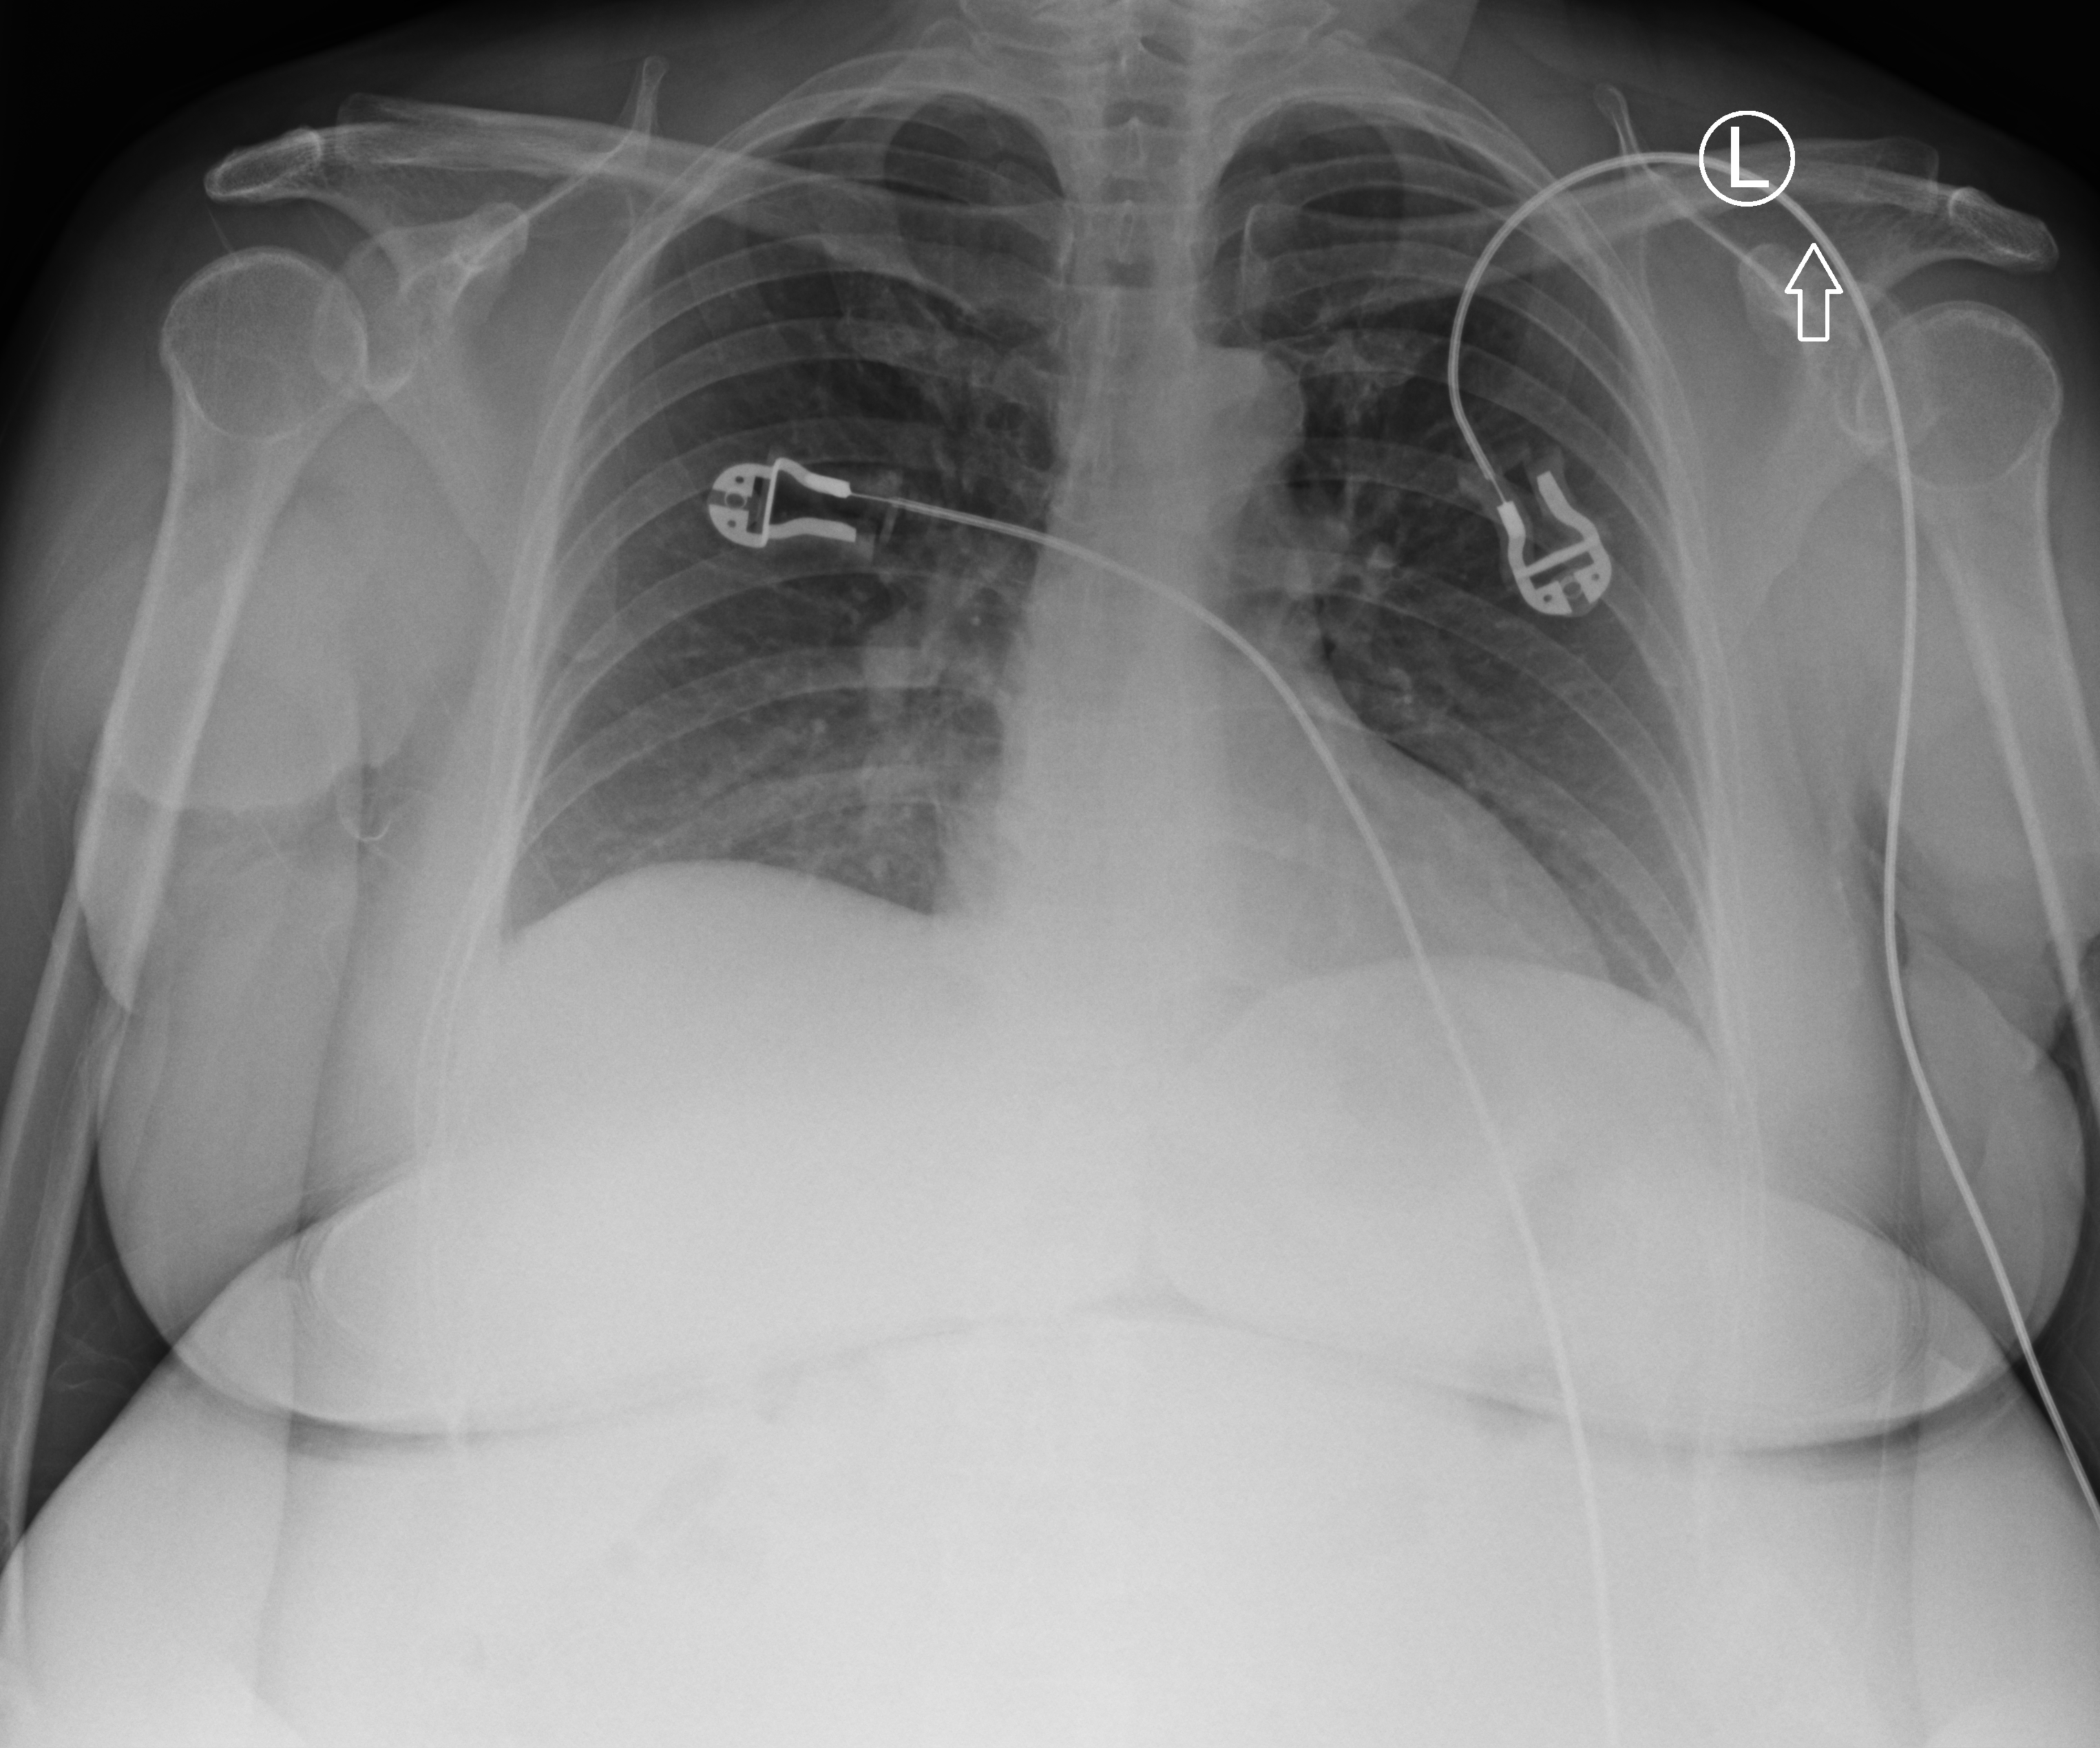
Portable chest radiograph; anteroposterior (AP) projection. Female patient hospitalised with COVID-19, age 18–59 years.
Hospital-stay facts (about this admission, not read from this image; timing relative to this image not recorded): mechanically ventilated during this hospital stay: no; admitted to intensive care during this hospital stay: no.